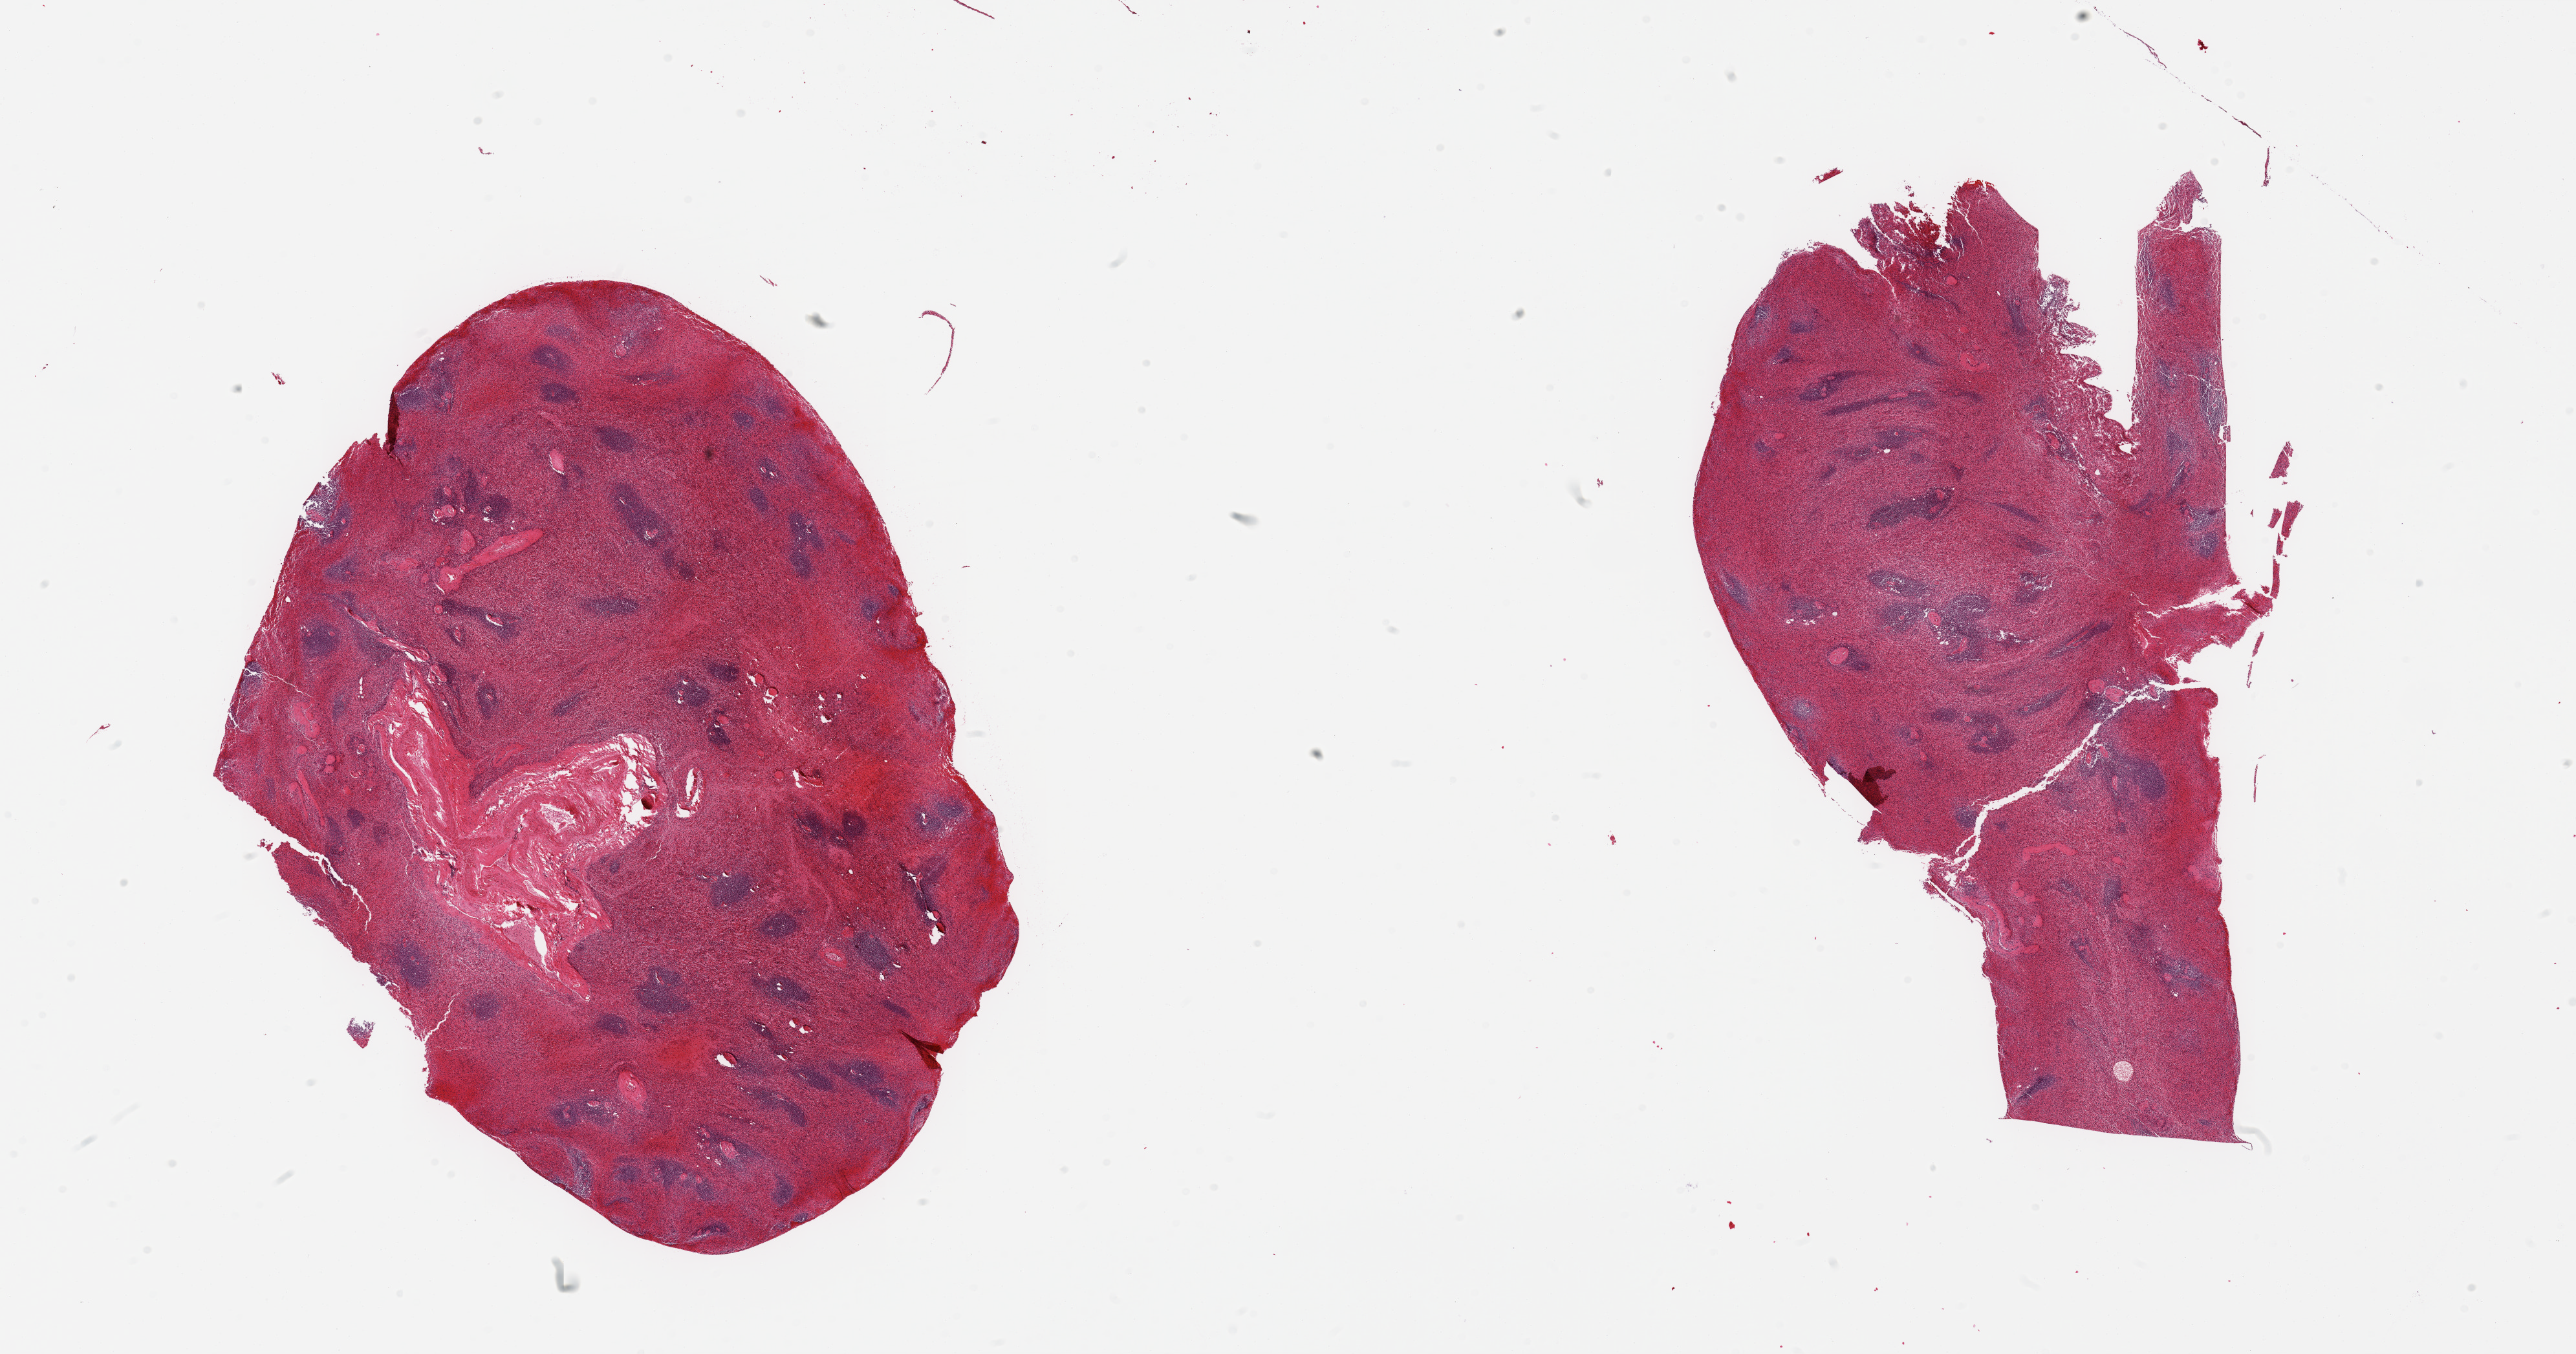
Whole-slide image, hematoxylin and eosin (H&E) stain, low-resolution overview of the scanned area, about 31.5 x 16.6 mm; PAXgene-fixed, paraffin-embedded tissue; target tissue: spleen; tissue donor sample. Male donor.
Review note (as recorded): 2 pieces, moderate congestion.